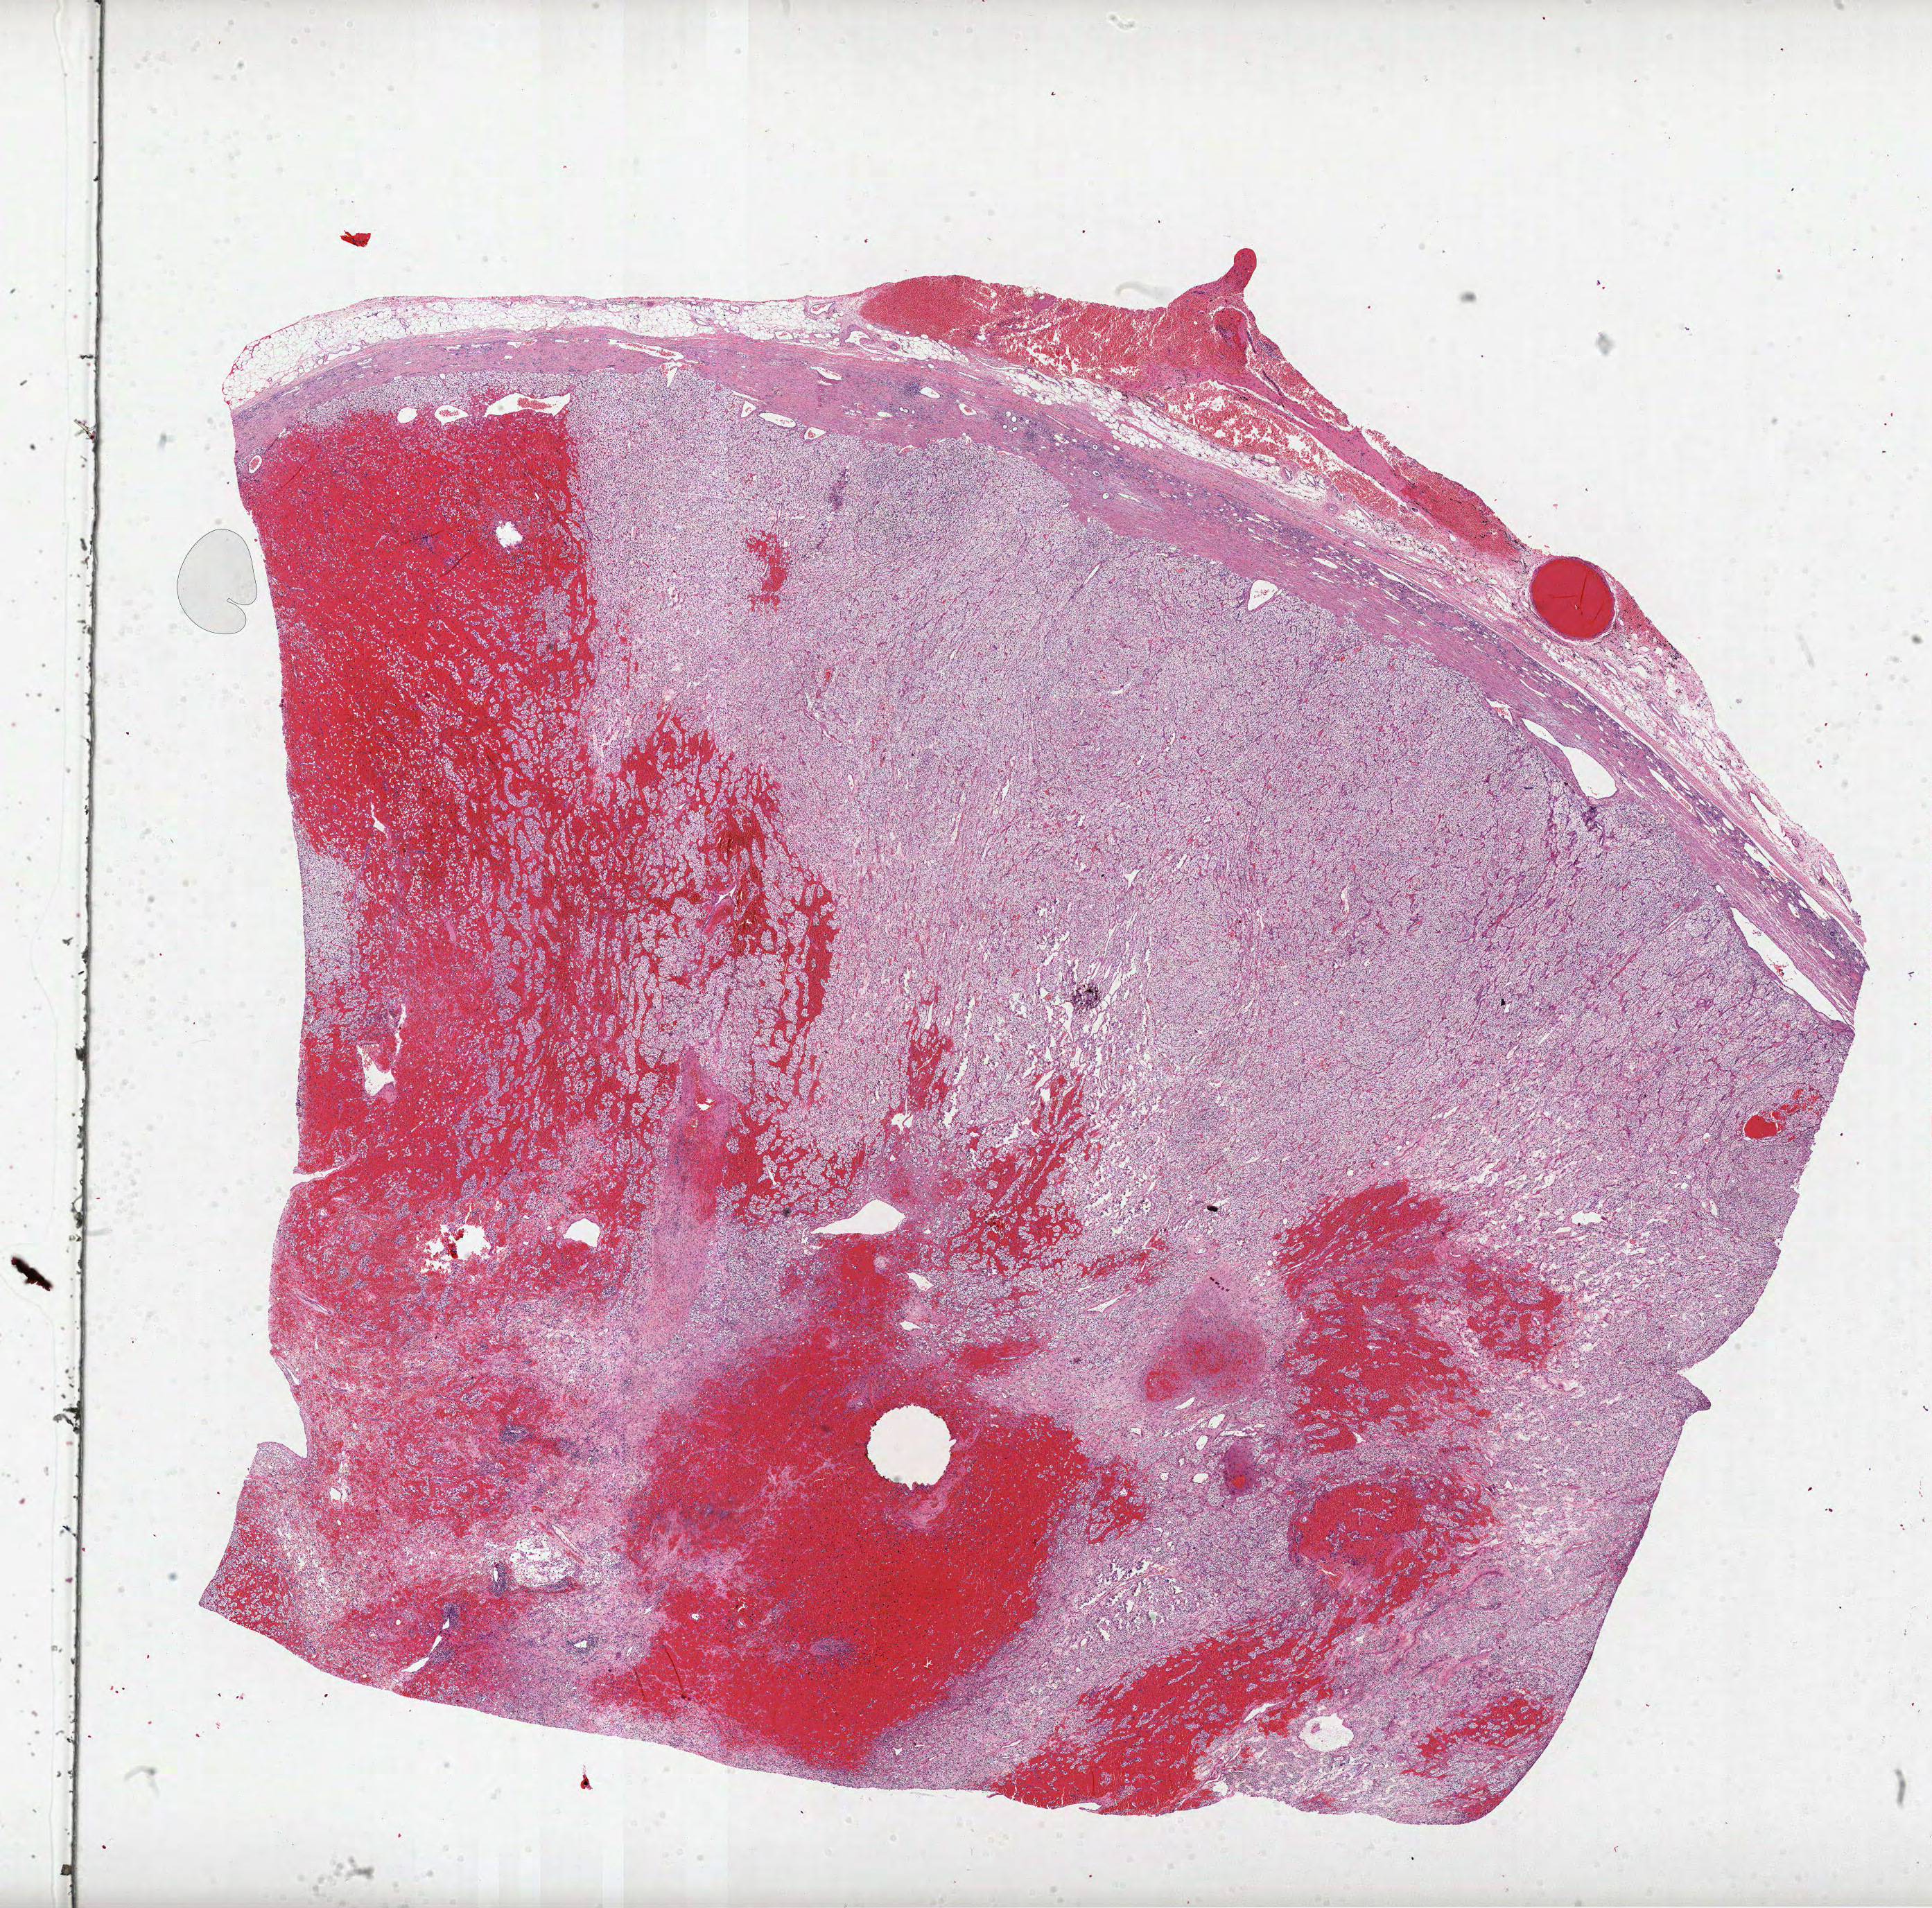
Digitized Hematoxylin and eosin (H&E) stained tissue section (whole slide), shown as a low-resolution overview of the whole scanned area (about 22.5 x 22.2 mm, slide scanned at 40x), formalin-fixed paraffin-embedded (FFPE) diagnostic section, kidney, primary tumour sample. Patient: female, age at initial diagnosis 61 years. Histologic grade: G2 (moderately differentiated).
AJCC pathologic stage: I (7th edition). TNM: T1b N0 M0. Diagnosis: Clear cell adenocarcinoma, NOS. Laterality: right.